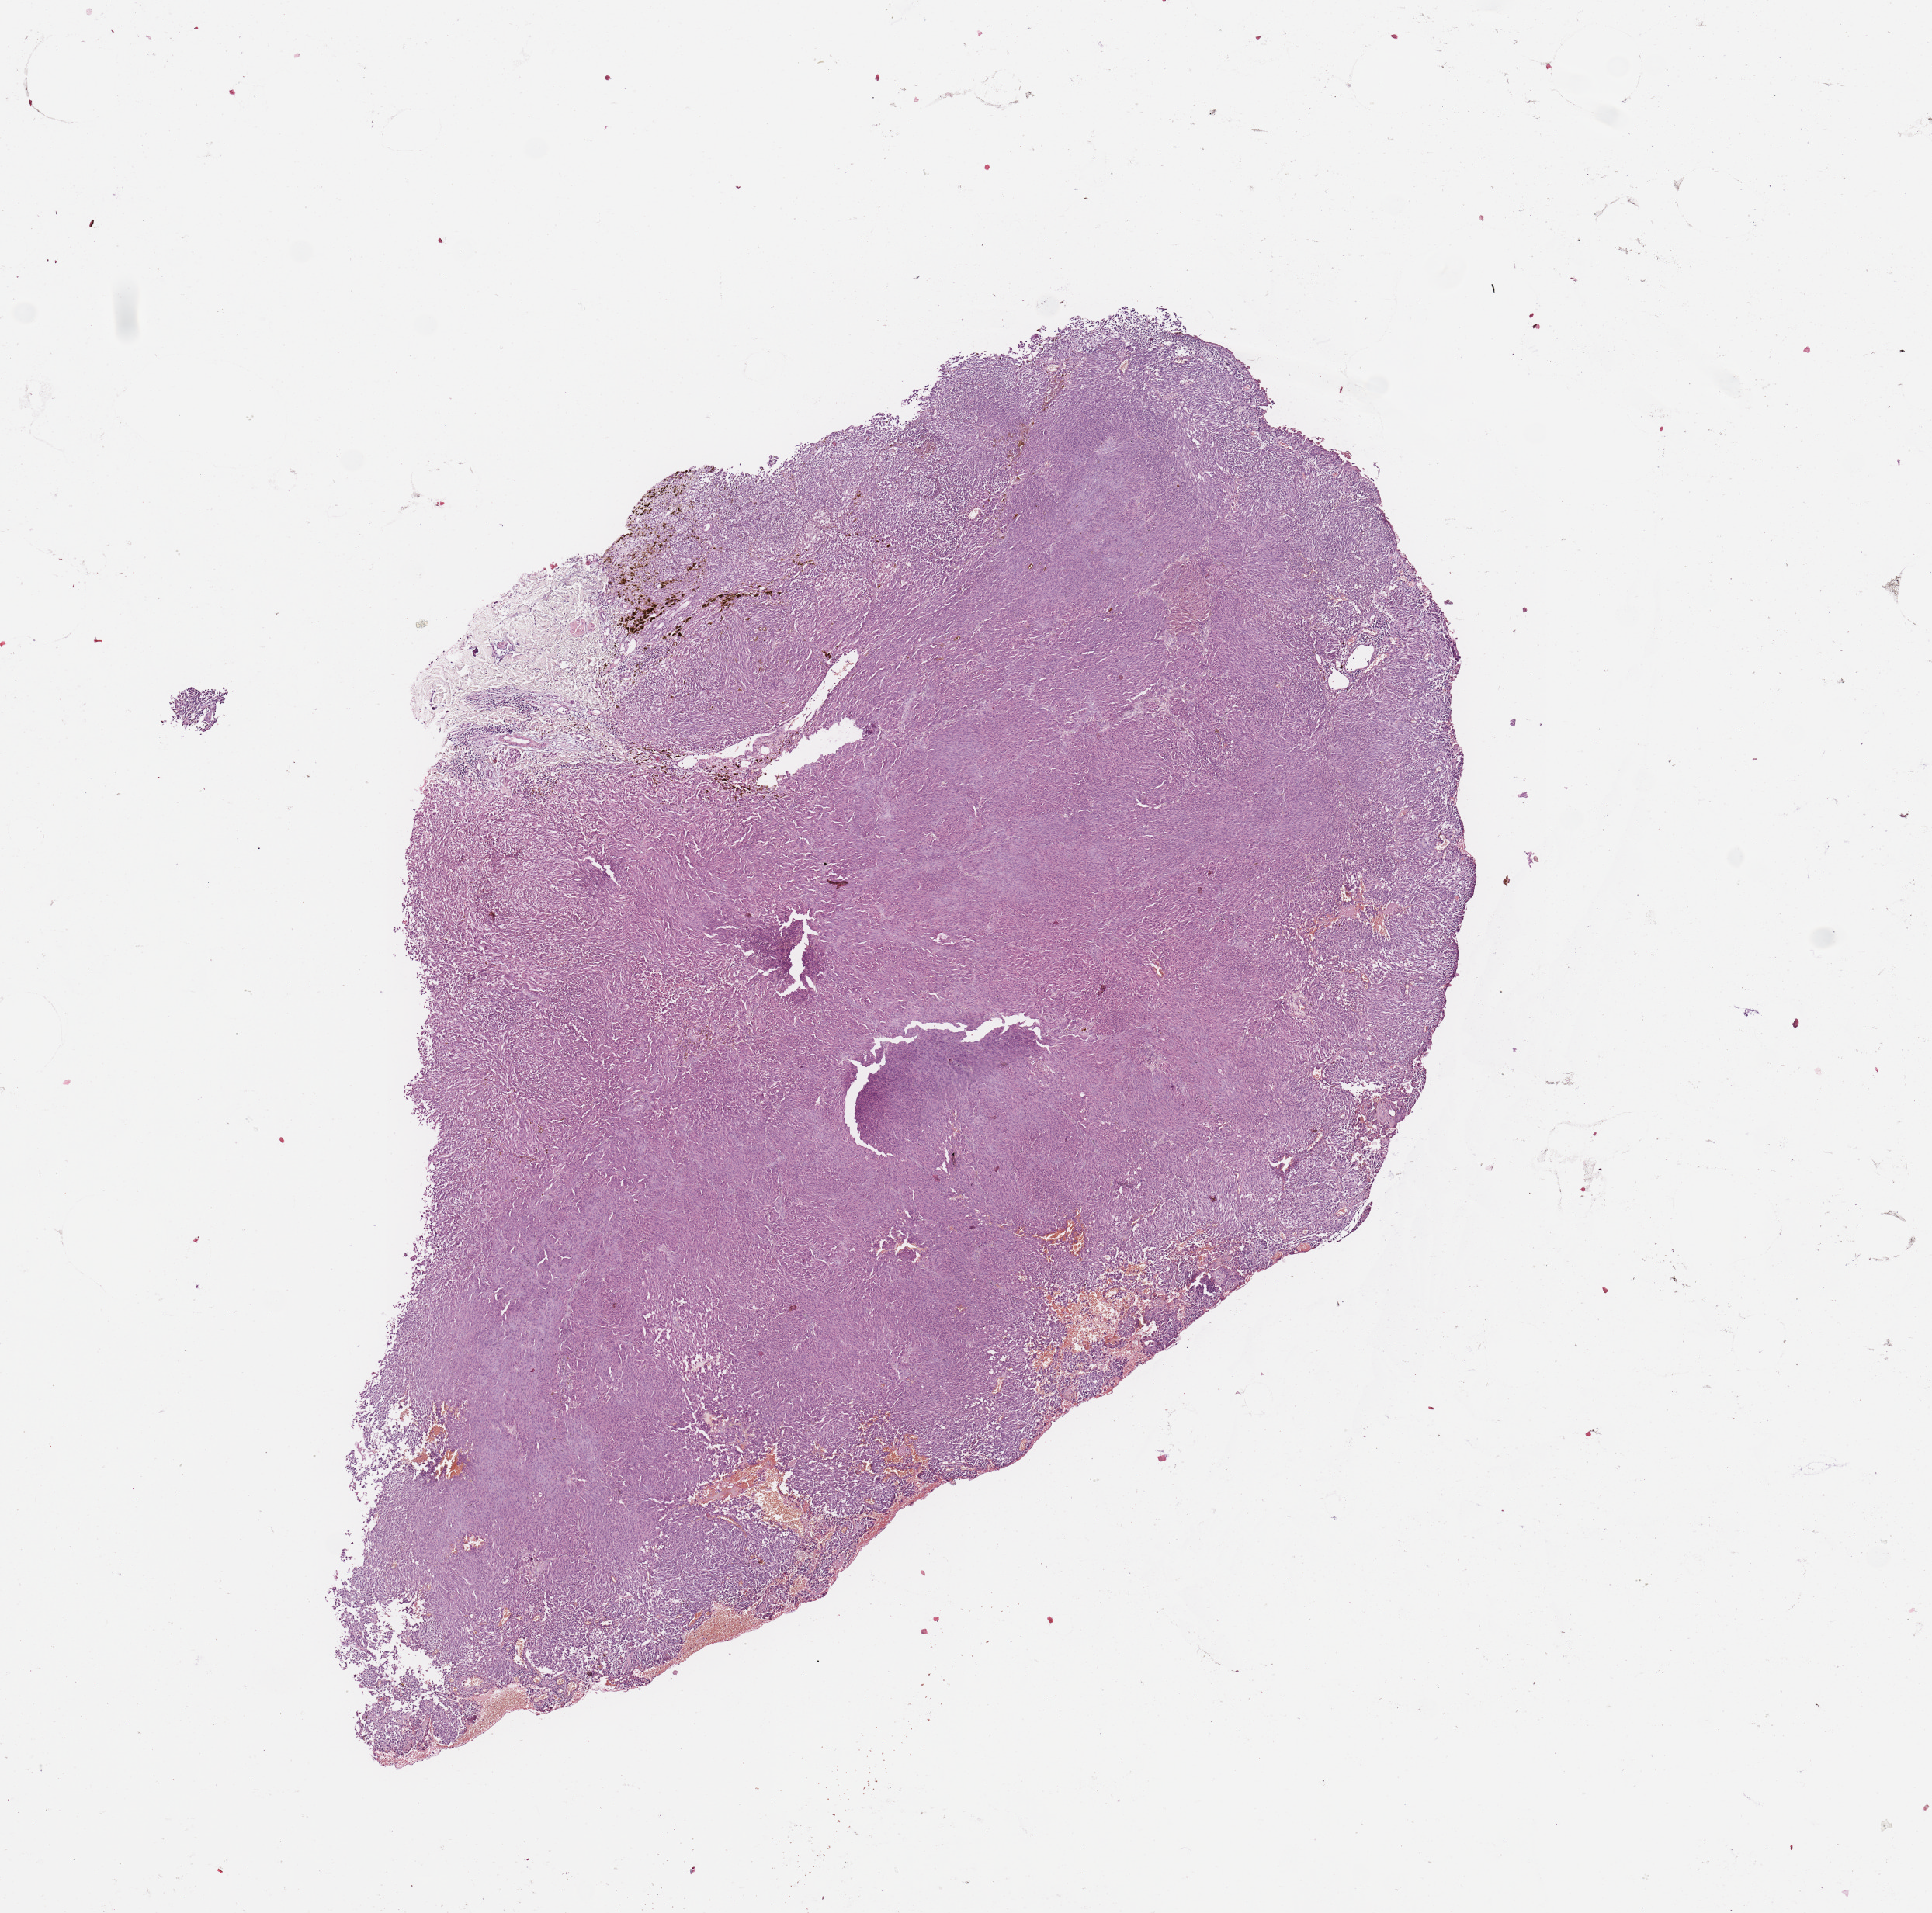
Whole-slide histology image, Hematoxylin and eosin (H&E) stained, low-resolution overview of the scanned area, about 9.8 x 9.7 mm (from a 20x scan); melanoma tumour tissue; sampled site not recorded. Patient: female, age 86 years.
AJCC pathologic stage: IIC. Histologic diagnosis: Malignant melanoma, NOS. Primary tumour site (as recorded): trunk.